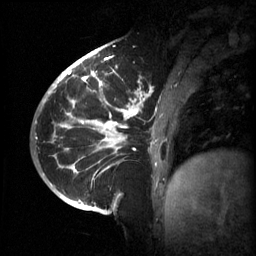
Breast MRI (dynamic contrast-enhanced), one sagittal slice; position 20 of 60 along the scan axis; 3 images stored at this slice position (order not interpretable as contrast timing); 1.5 T; TE 4.2 ms, TR 11 ms; 2 mm slice thickness; 256 × 256 image matrix, field of view 220 × 220 mm. Patient: female, 51 years.
Outlined on this slice (semi-automatically segmented with operator editing):
- analysis volume of interest (the breast-tissue region the enhancement analysis was run in; not a lesion): bounding box [x1, y1, x2, y2] px = [63, 80, 187, 201]
- tumour enhancement mask (voxels above the 70 % enhancement threshold inside the analysis volume of interest): [65, 80, 180, 185]